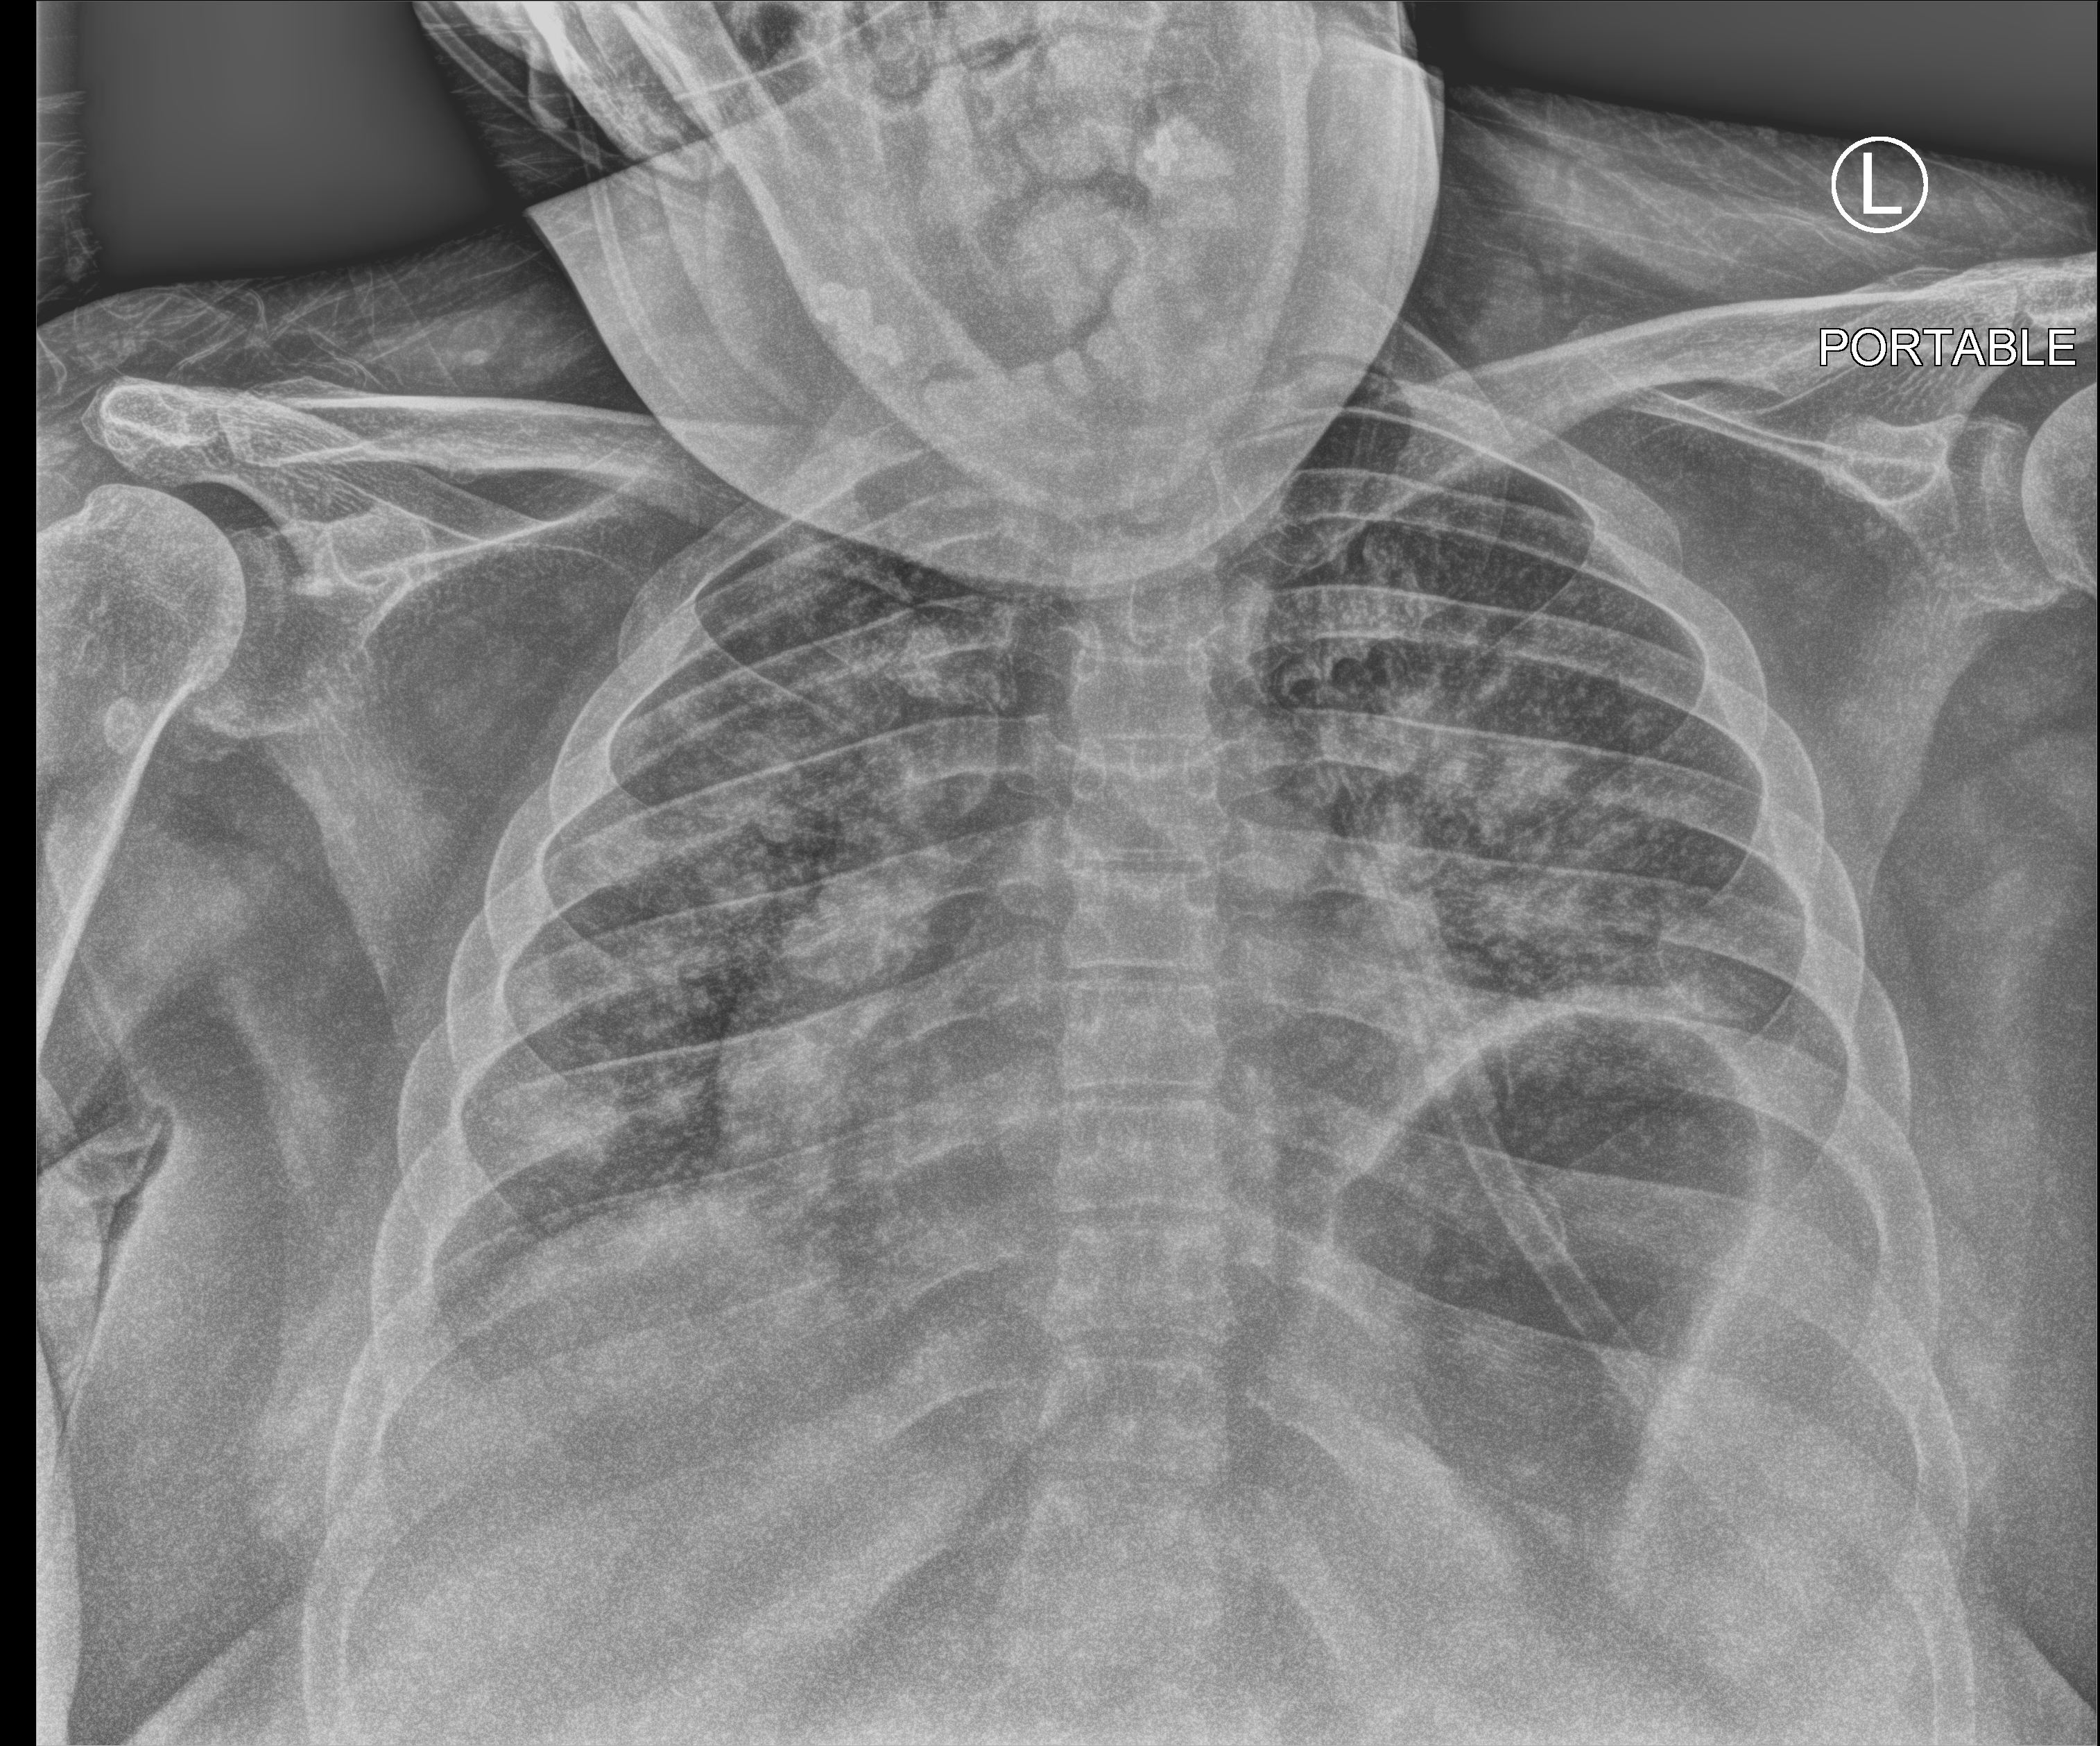
Chest X-ray (portable); anteroposterior (AP) projection. Female patient hospitalised with COVID-19, age 18–59 years.
Hospital-stay facts (about this admission, not read from this image; timing relative to this image not recorded): mechanically ventilated during this hospital stay: no.